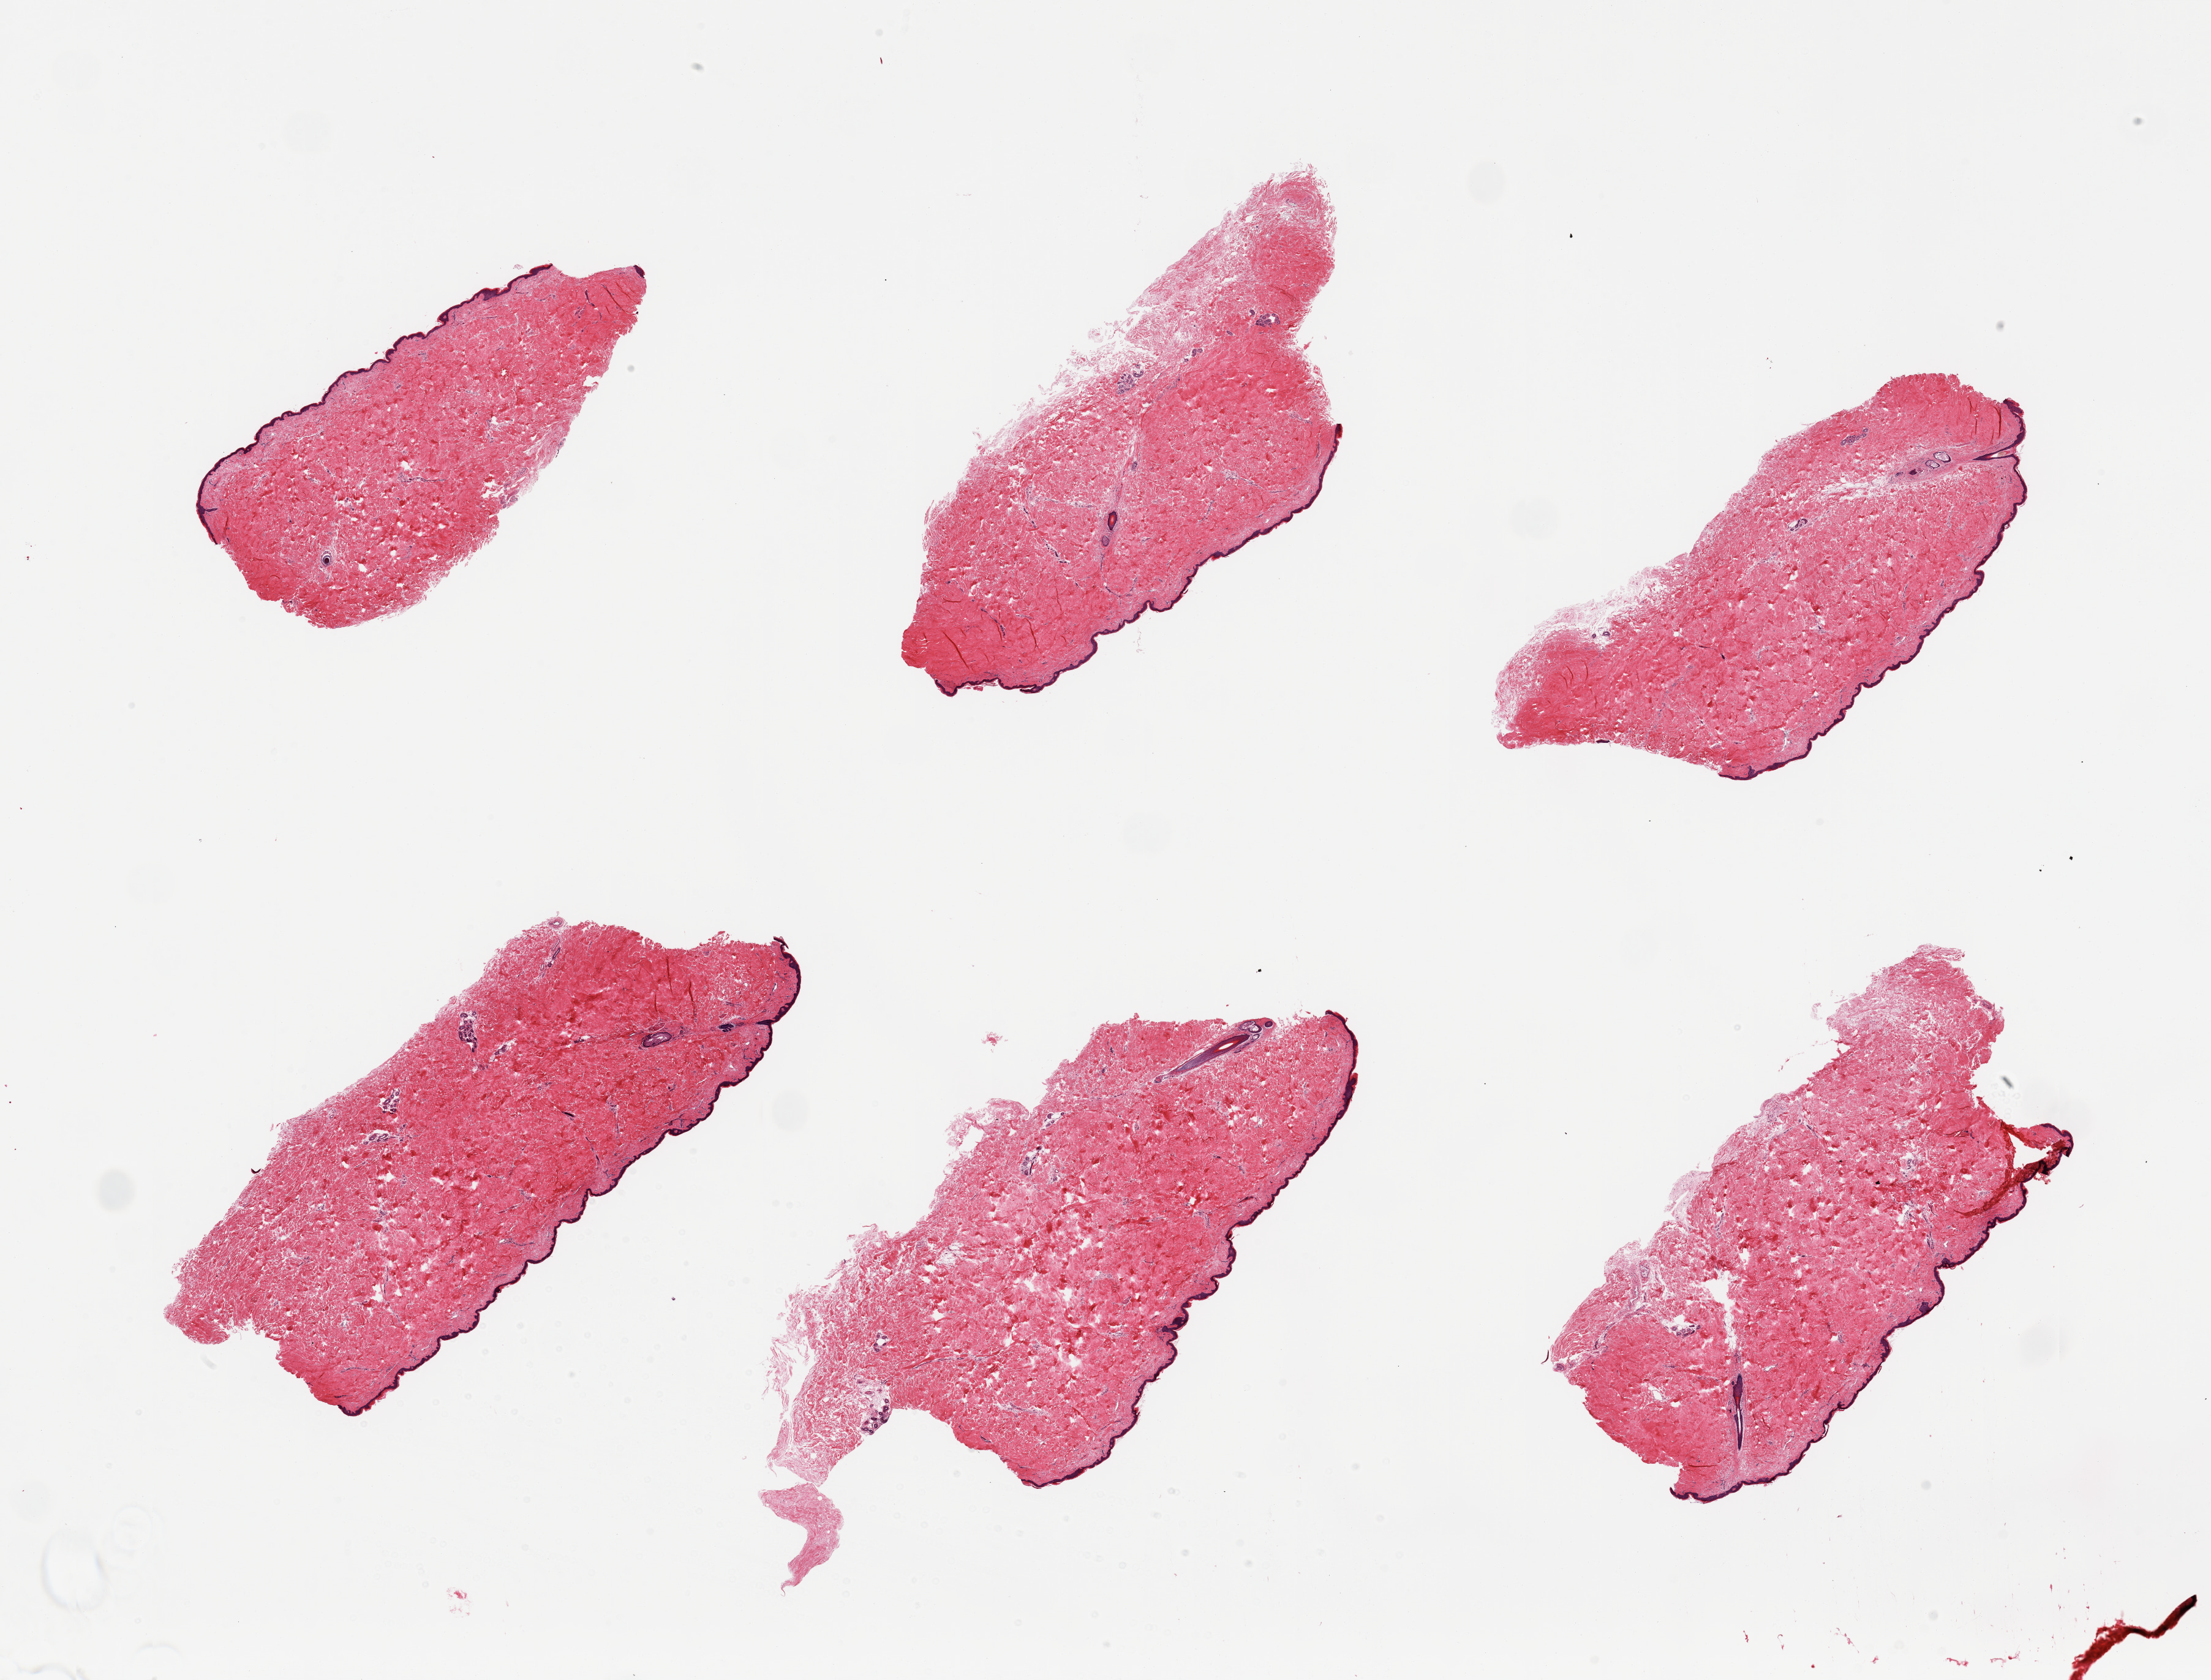
Whole-slide image, H&E stain, low-resolution overview of the scanned area, about 28.5 x 21.7 mm, PAXgene-fixed paraffin-embedded (PFPE) section, target tissue: skin of suprapubic region, tissue donor sample. Donor sex: male.
* review note (as recorded): 6 pieces, minimal dermal fat; squamous epithelium is 35-40 microns